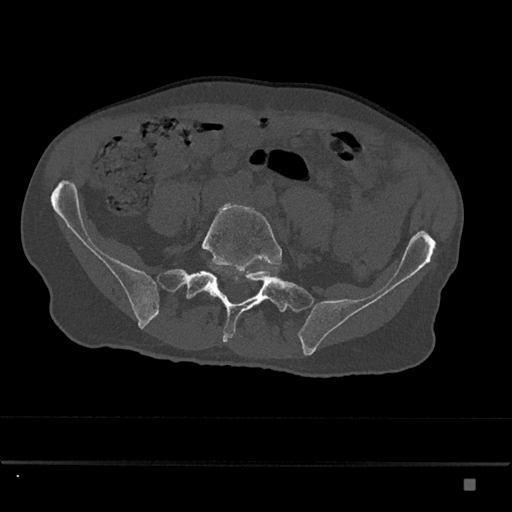
CT including the spine, one axial slice. Position 253 of 797 along the scan axis. Reconstruction kernel Br40s/3. Bone window (W 1800 / L 400 HU). 0.5 mm slice thickness. 512 × 512 image matrix, field of view 390 × 390 mm. Patient: male, 72 years. Case-level facts recorded for this patient, not image findings: primary cancer: prostate.
Structures marked on this image (semi-automatically segmented with operator editing):
- L5 vertebra: bounding box <202,203,282,294> (left, top, right, bottom; pixels)